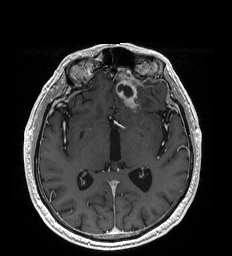
Brain MRI from a brain-tumour surgery series, one axial slice; position 107 of 192 along the scan axis; T1-weighted post-contrast; 1 mm slice thickness; 232 × 256 image matrix, field of view 227 × 250 mm. Case-level facts recorded for this patient, not image findings: histopathology: Glioblastoma; WHO grade: 4; IDH mutation: no.
Outlined on this slice (expert manual segmentation):
- tumour: bounding box <118,85,138,108> (left, top, right, bottom; pixels)